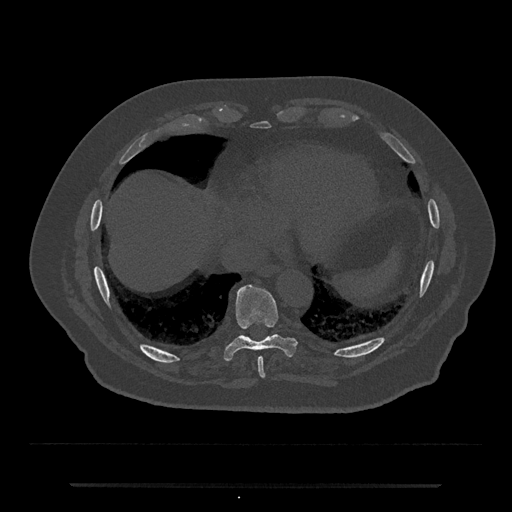
CT including the spine, one axial slice. Position 759 of 797 along the scan axis. Reconstruction kernel Br40s/3. Bone window (W 1800 / L 400 HU). 0.5 mm slice thickness. 512 × 512 image matrix. Male patient, age 80 years. Case-level facts recorded for this patient, not image findings: primary cancer: prostate.
Structures marked on this image (semi-automatically segmented with operator editing):
- T8 vertebra: box from (x=257, y=357) to (x=265, y=378) px
- T9 vertebra: (x=224, y=283)–(x=295, y=360)